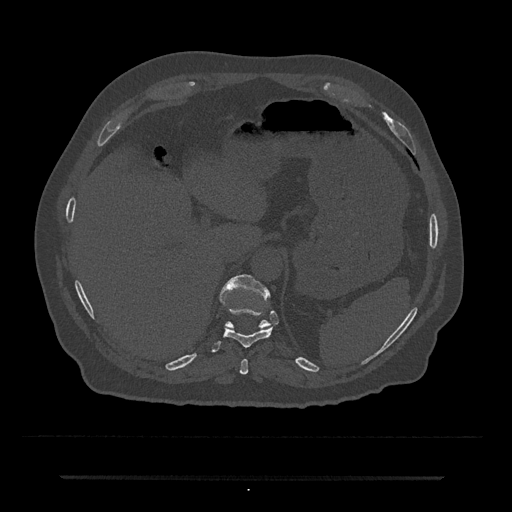
CT including the spine, one axial slice. Slice 220 of 797 in the series (ordered by position). 120 kVp. Bone window (W 1800 / L 400 HU). 512 × 512 image matrix, field of view 437 × 437 mm. Male patient, age 69 years. Case-level facts recorded for this patient, not image findings: primary cancer: prostate.
Outlined on this slice (semi-automatically segmented with operator editing):
- T10 vertebra: box from (x=211, y=308) to (x=273, y=353) px
- T11 vertebra: (x=219, y=274)–(x=271, y=330)
- T9 vertebra: (x=240, y=359)–(x=248, y=375)